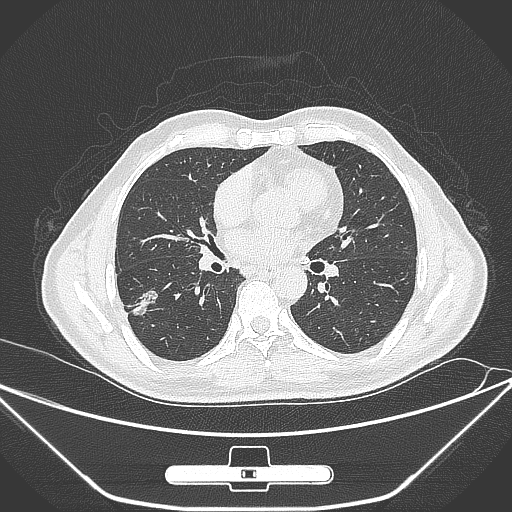
Chest CT, one axial slice; position 143 of 310 along the scan axis; 120 kVp; lung window (W 1500 / L -600 HU); 1 mm slice thickness; 512 × 512 image matrix, field of view 398 × 398 mm. Patient: male, 71 years. Case-level facts recorded for this patient, not image findings: clinical TNM (as recorded): T1c N0 M0.
Structures marked on this image (bounding box drawn by a radiologist):
- lung tumour (recorded histology: adenocarcinoma): bounding box [x1, y1, x2, y2] px = [131, 280, 155, 318]